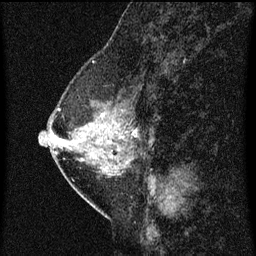
Breast MRI (dynamic contrast-enhanced), one sagittal slice; slice 24 of 60 in the series (ordered by position); dynamic contrast-enhanced series, image 2 of 3 at this slice position (ordered by acquisition); 1.5 T; TE 4.2 ms, TR 8 ms; 2 mm slice thickness; 256 × 256 image matrix, field of view 180 × 180 mm. Female patient, age 47 years.
Annotated regions visible in this slice (semi-automatically segmented with operator editing):
- analysis volume of interest (the breast-tissue region the enhancement analysis was run in; not a lesion): bounding box <54,84,146,187> (left, top, right, bottom; pixels)
- tumour enhancement mask (voxels above the 70 % enhancement threshold inside the analysis volume of interest): <56,110,132,161>